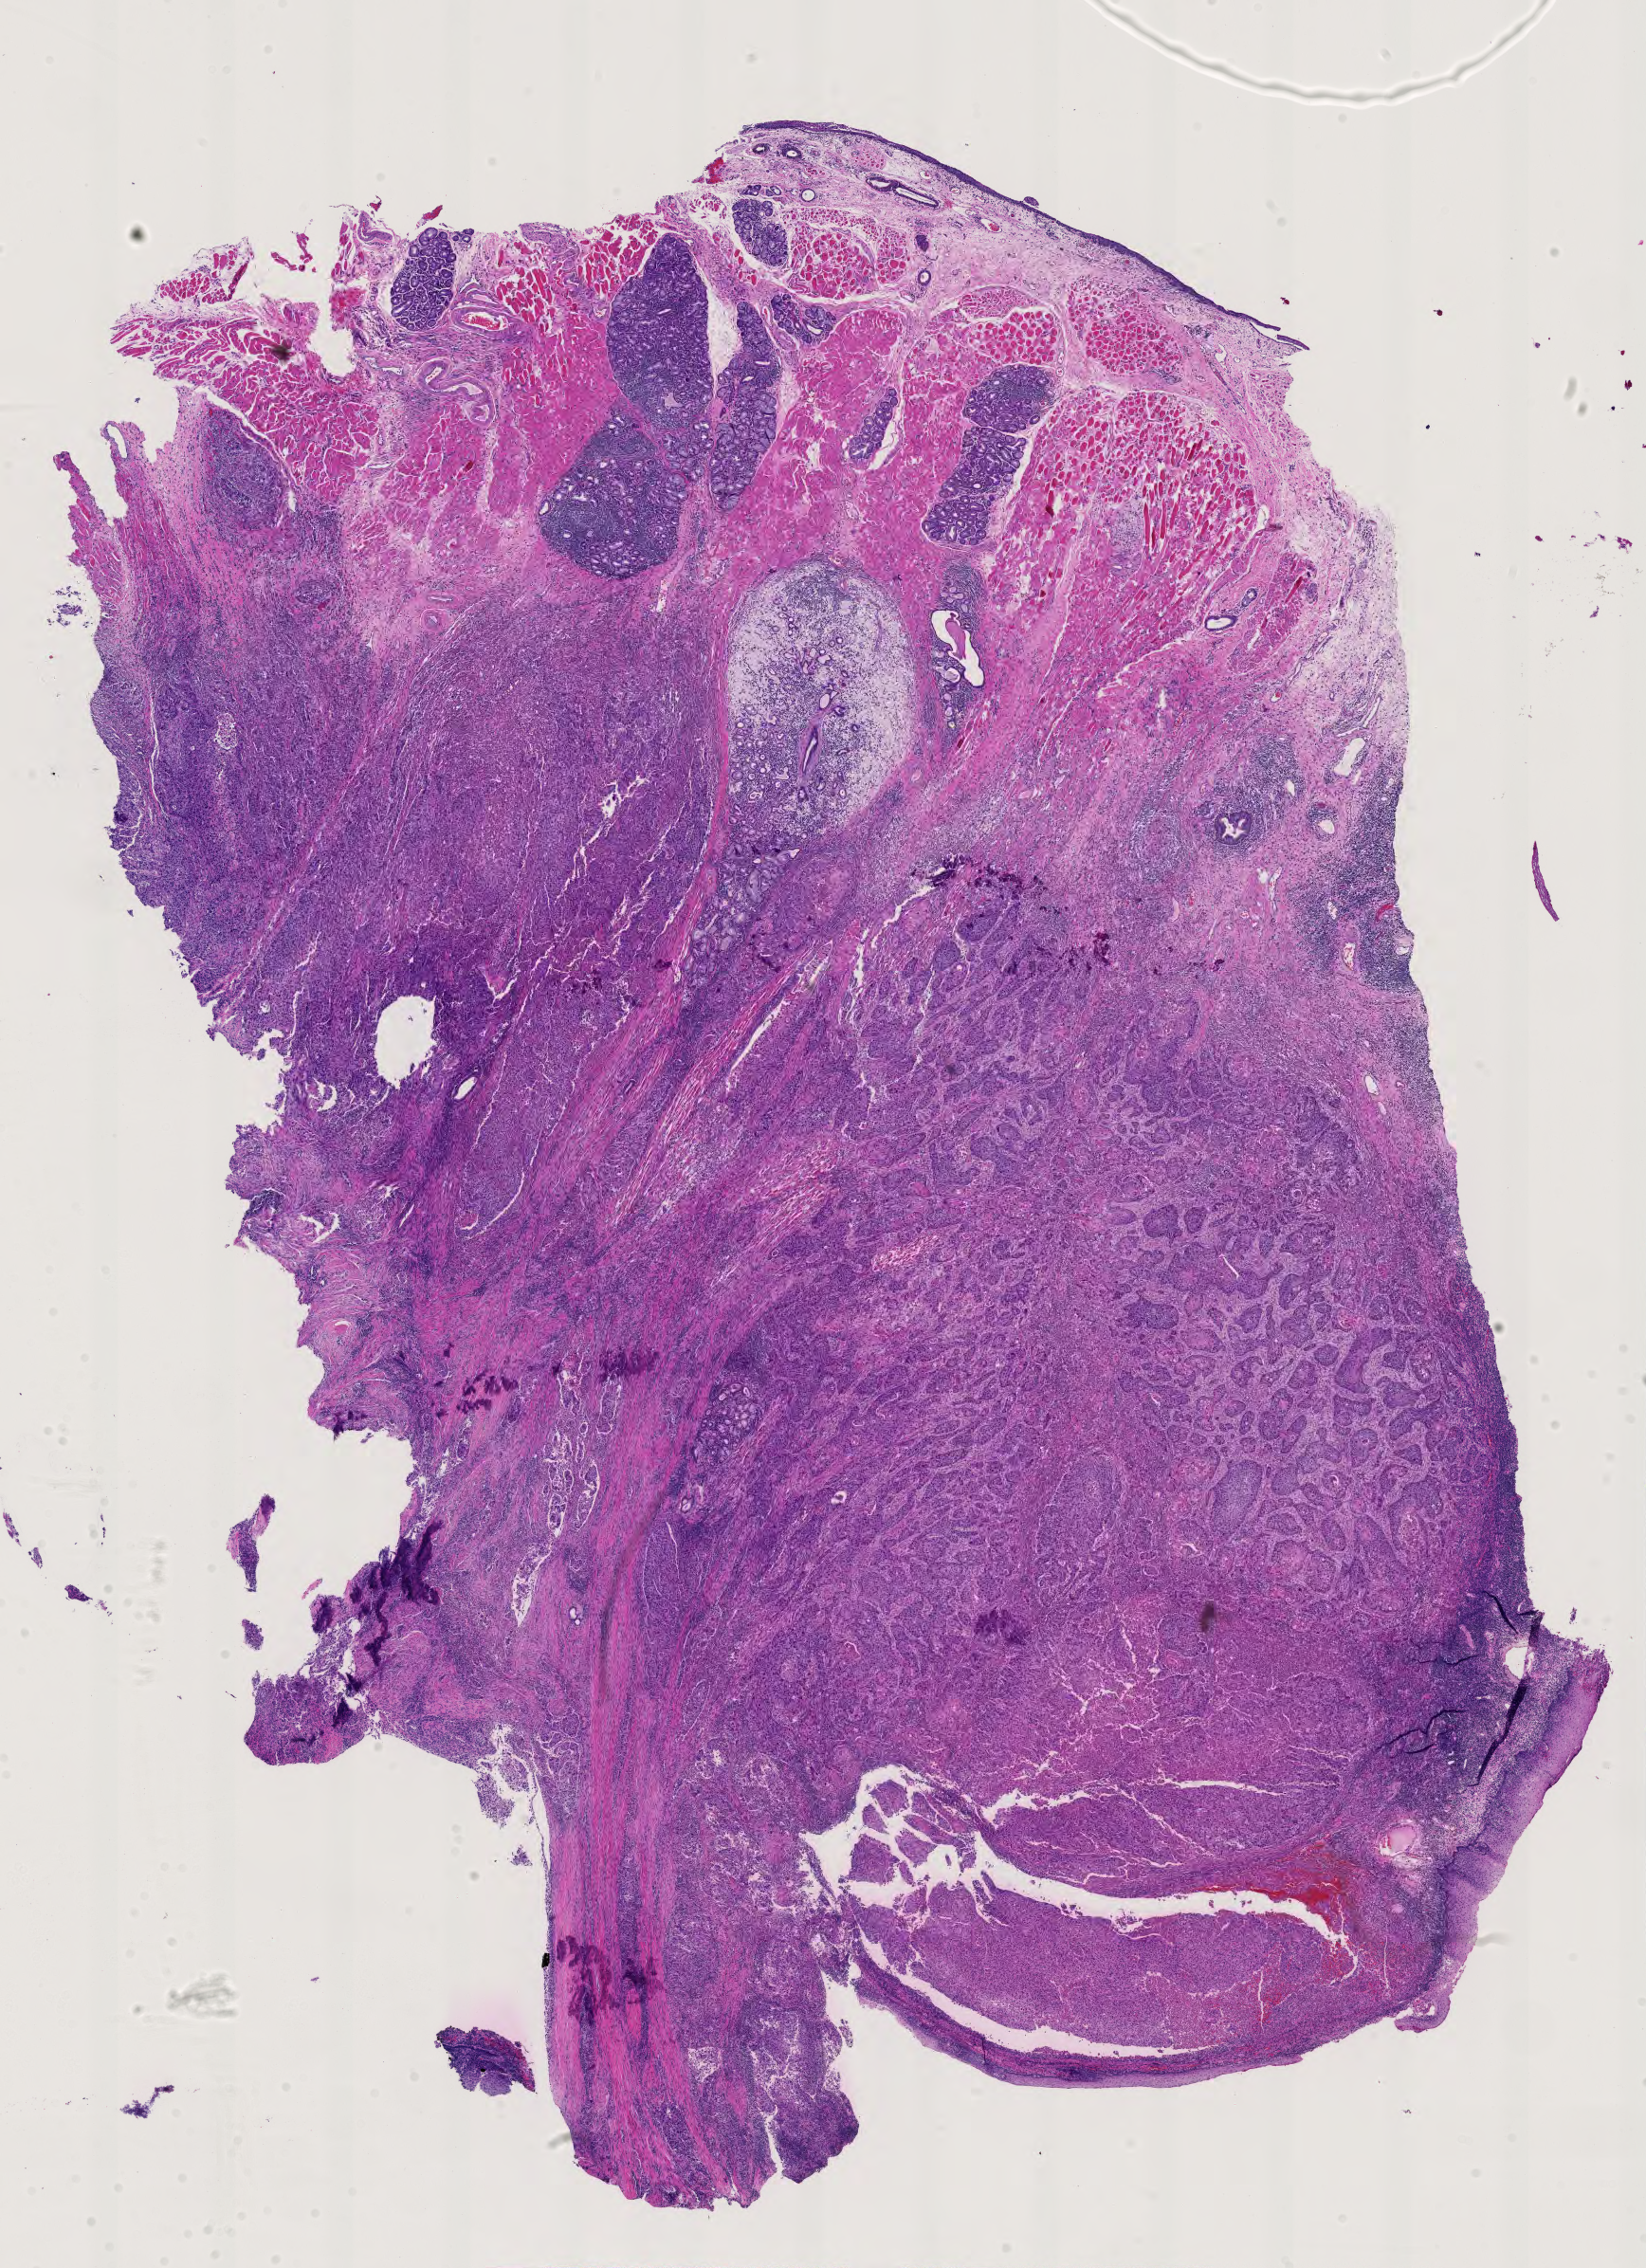
Digitized Hematoxylin and eosin (H&E) stained tissue section (whole slide) — low-resolution overview of the scanned area, about 12.6 x 17.3 mm (from a 40x scan), formalin-fixed paraffin-embedded (FFPE) diagnostic section, sample: primary tumour, head and neck. Patient: female, age at initial diagnosis 62 years. Histologic grade: G2 (moderately differentiated).
Laterality: right. AJCC pathologic stage: IVA. Lymph nodes positive (case pathology): 1 of 67 examined. Histologic diagnosis: Squamous cell carcinoma, NOS (hypopharynx, NOS).